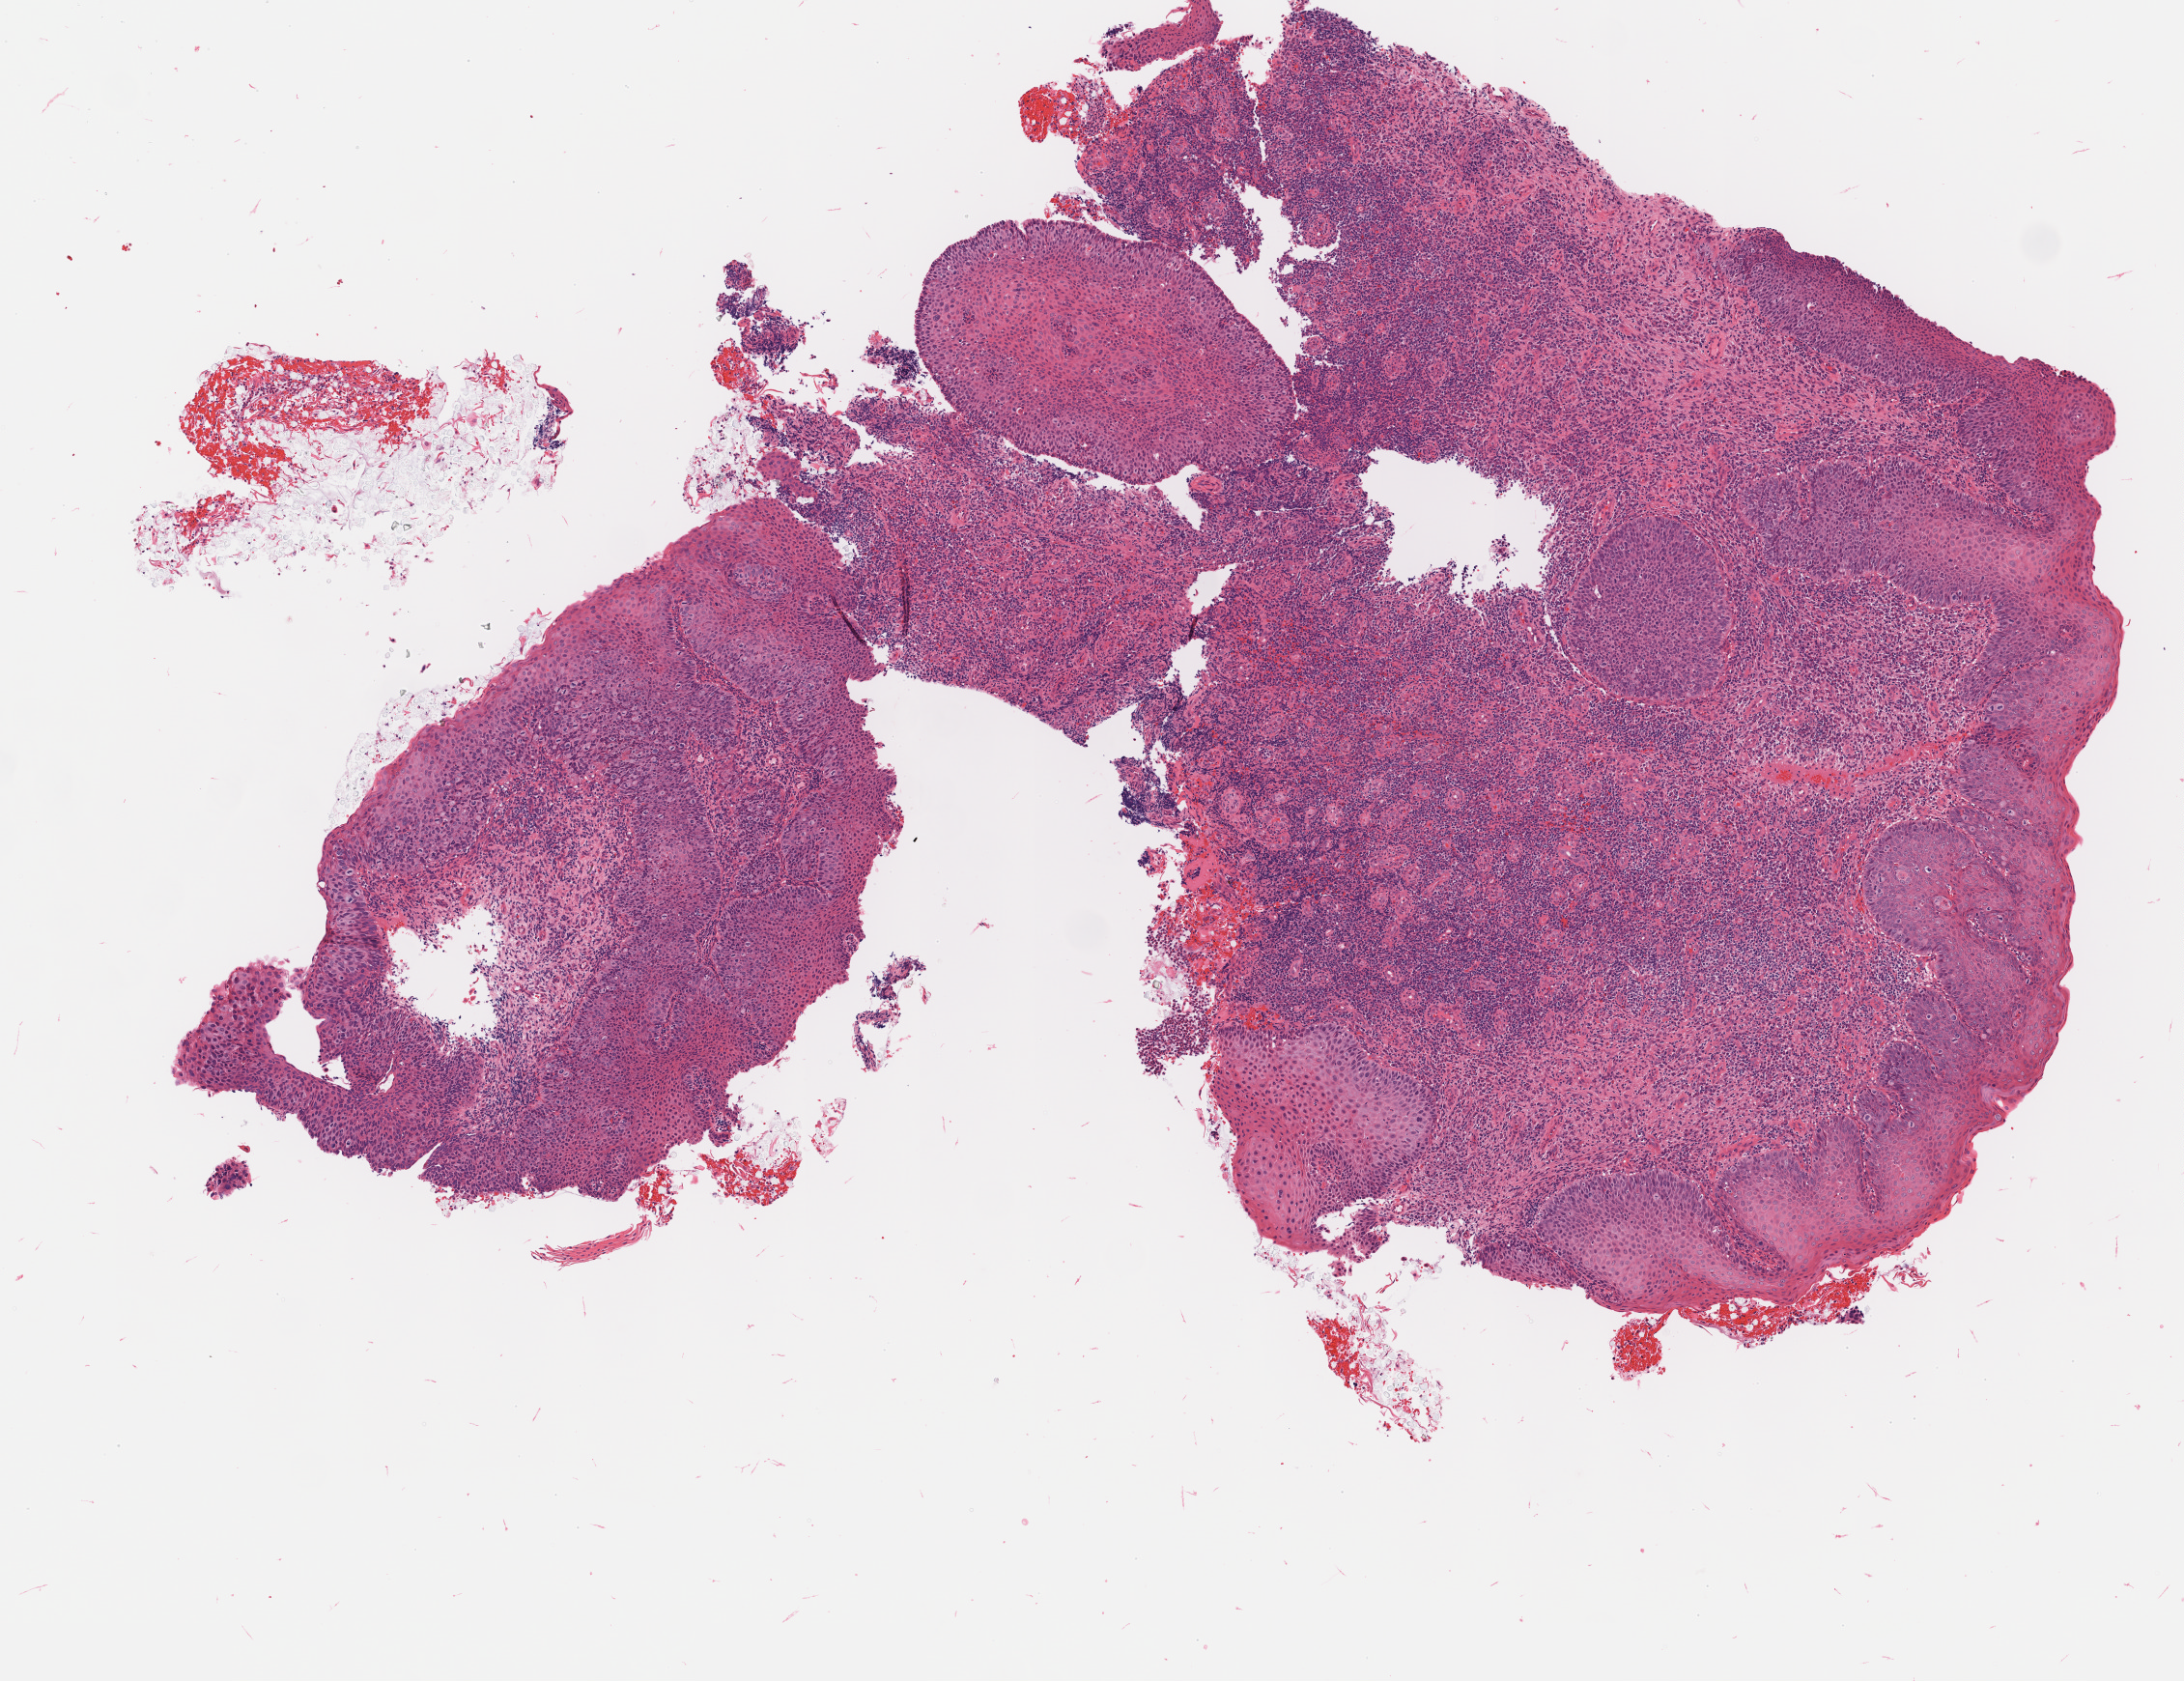
Whole-slide image, H&E stain, low-resolution overview of the scanned area, about 4.5 x 3.5 mm. Female patient, 43 years old.
Specimen: tumor tissue; site: cervix.